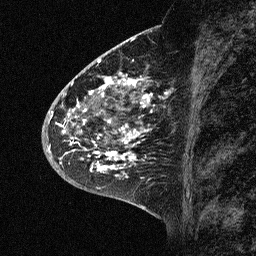
Breast MRI (dynamic contrast-enhanced), one sagittal slice. Position 25 of 64 along the scan axis. Dynamic contrast-enhanced study with each time point stored as its own series, time point 2 of 3 at this slice position (early post-contrast, ordered by acquisition time). 1.5 T. TE 4.5 ms, TR 11 ms. 2.06 mm slice thickness. 256 × 256 image matrix, field of view 200 × 200 mm. Female patient, age 46 years. From the clinical record (not read from this slice): setting: breast cancer imaged before/during neoadjuvant chemotherapy; receptor status: HER2-positive.
Outlined on this slice (semi-automatic segmentation, software-assisted and operator-edited):
- analysis volume of interest (the breast-tissue region the enhancement analysis was run in; not a lesion): bounding box (x1, y1, x2, y2) in pixels: (43, 72, 176, 177)
- tumour enhancement mask (voxels above the 90 % enhancement threshold inside the analysis volume of interest): (55, 76, 150, 177)